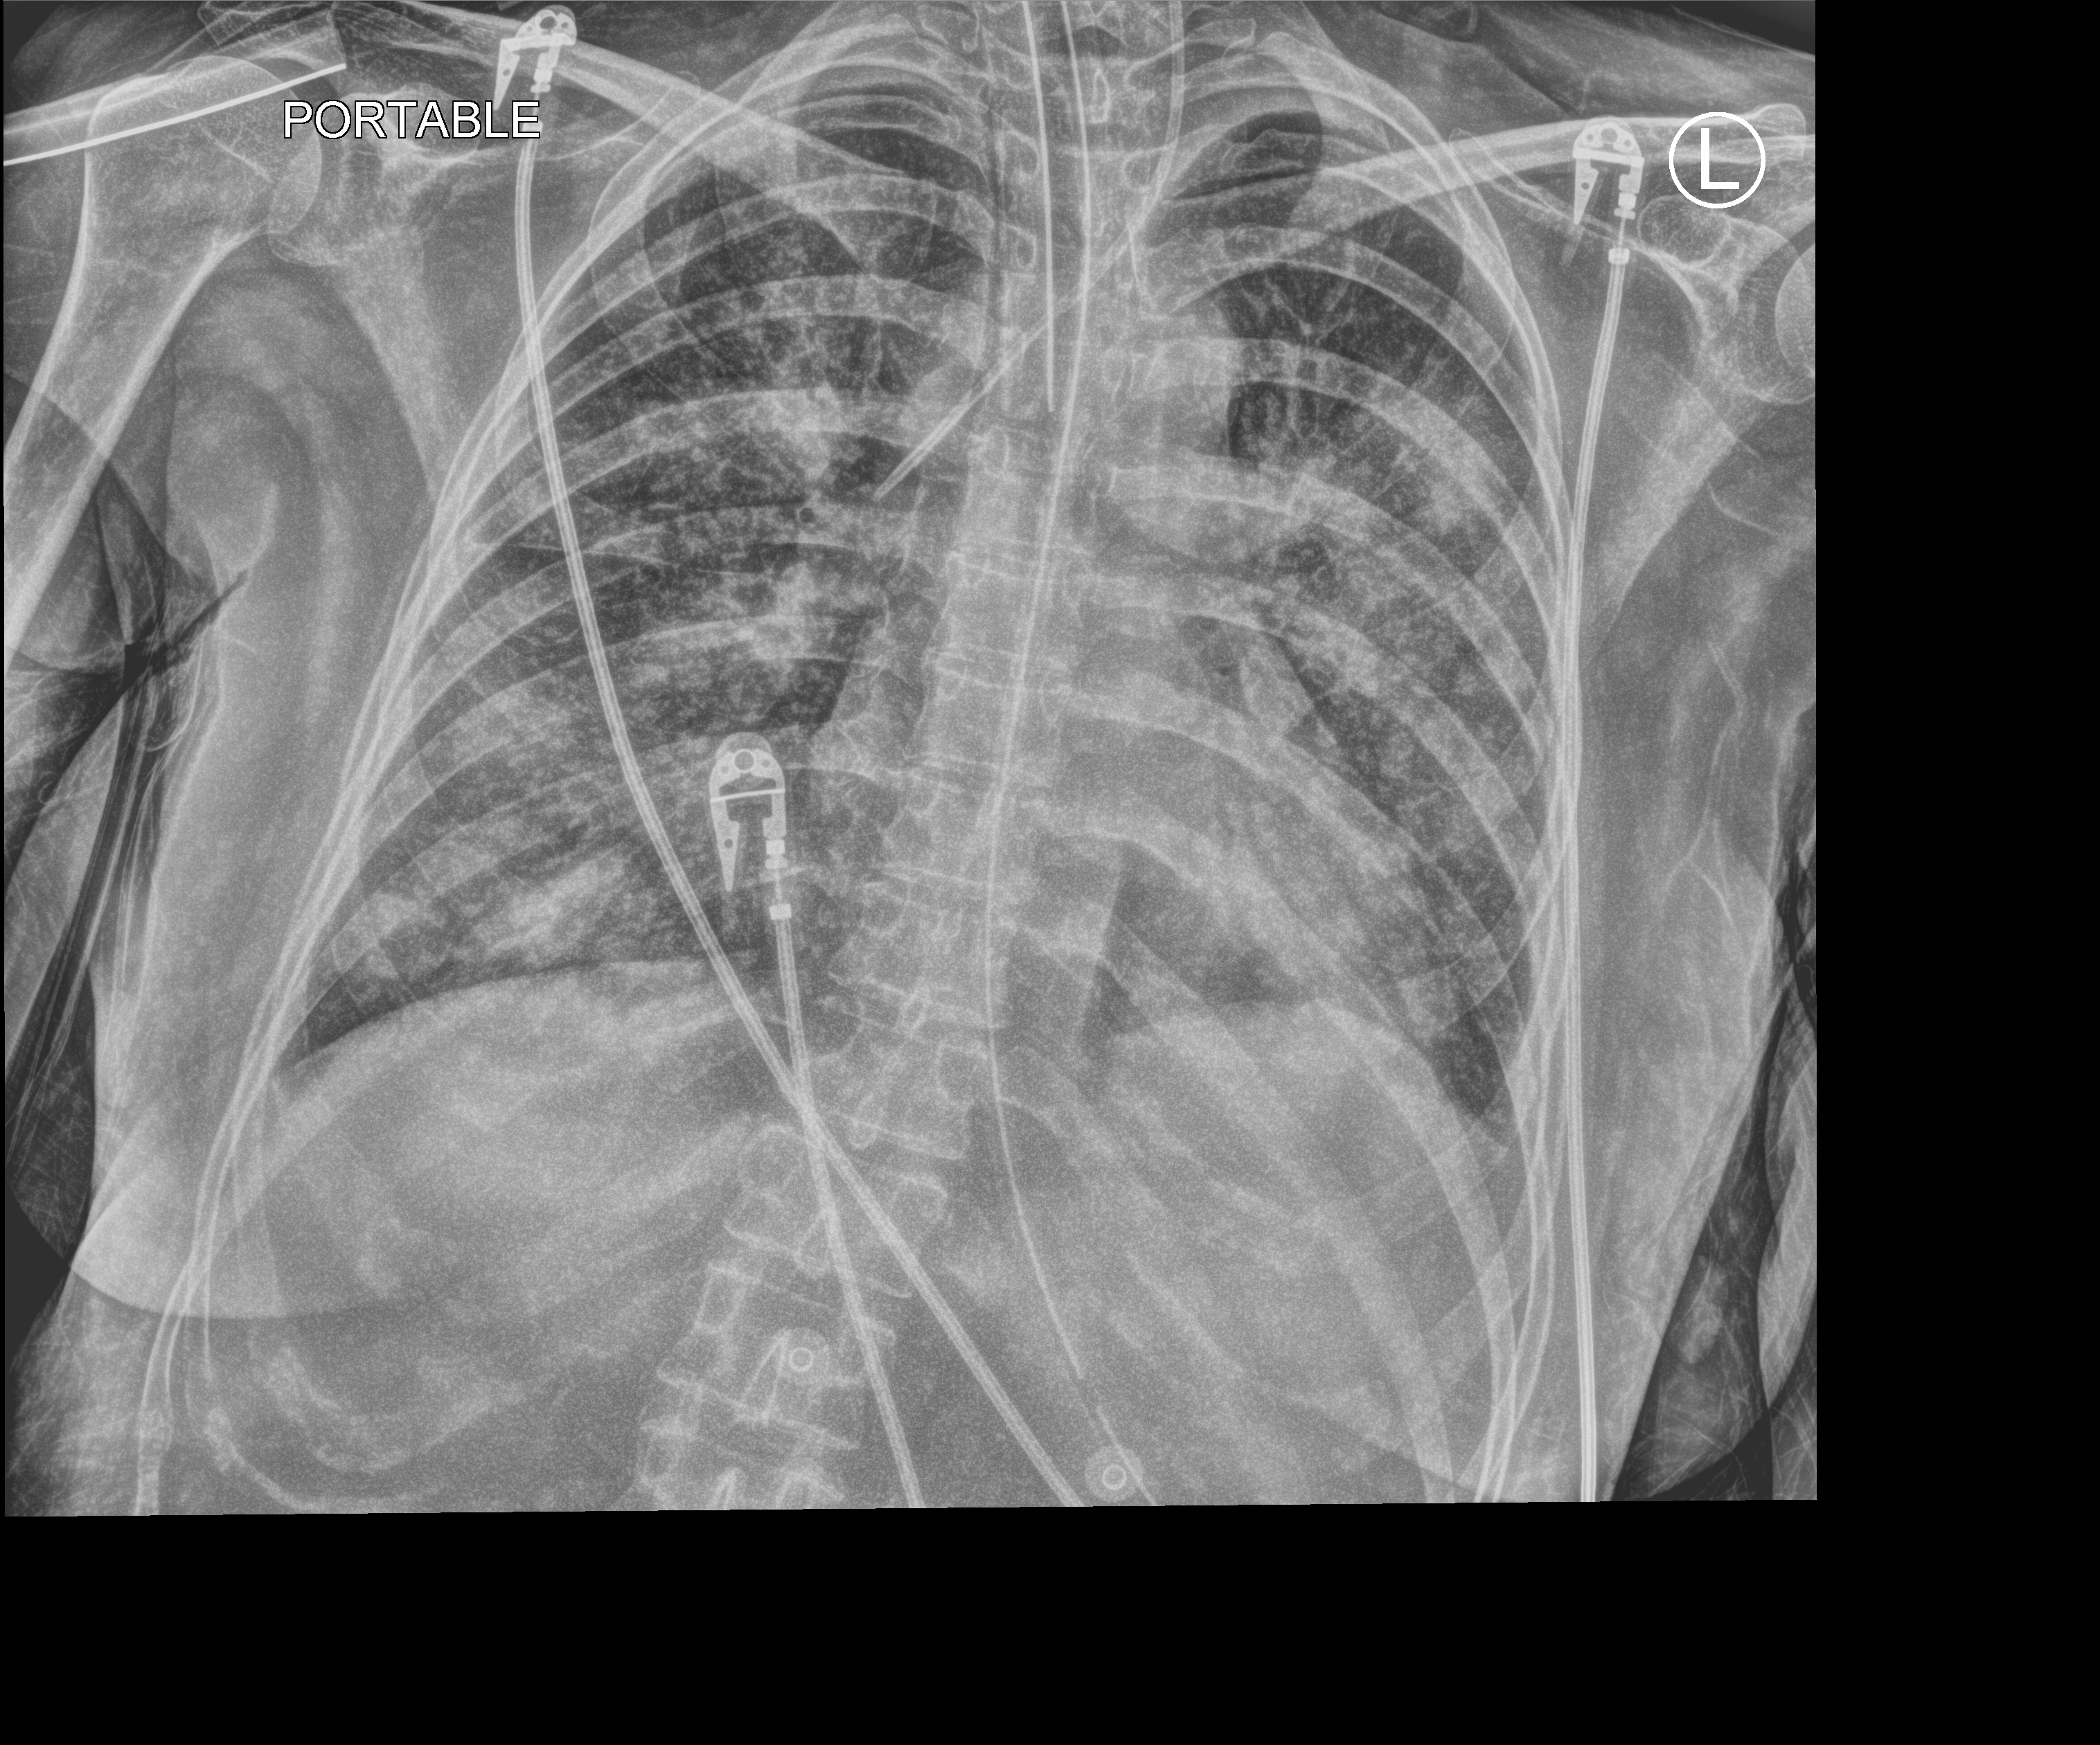
Portable chest radiograph; anteroposterior (AP) projection. Patient hospitalised with COVID-19, aged 18–59 years.
From the hospital-stay record, not from the radiograph (when in the stay this image was taken is not recorded): mechanically ventilated during this hospital stay: yes; length of hospital stay: 10 days; admitted to intensive care during this hospital stay: yes.